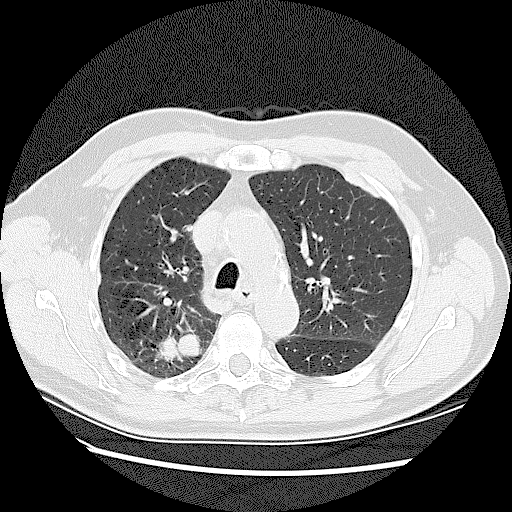
Chest CT (low-dose screening protocol), one axial image. Baseline screening round. Lung window (W 1500 / L -600 HU). 2.5 mm slice thickness. Slice 40 of 128 in the series. Male participant, aged 72 years at enrolment. Current smoker at enrolment.
- Expert reader's lesion annotation, bounding box <141,313,213,377> (left, top, right, bottom; pixels).
- The screening reader recorded 2 non-calcified nodules or masses ≥4 mm on this exam; which of them this box marks is not recorded.
- Official screen result: positive, change unspecified: nodule(s) >= 4 mm or enlarging nodule(s), mass(es), or other non-specific abnormalities suspicious for lung cancer.